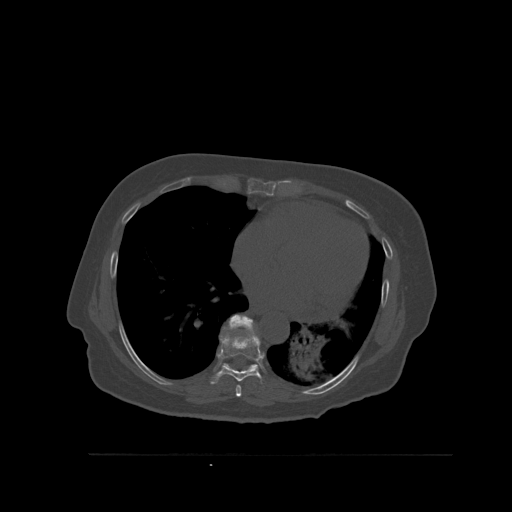
CT including the spine, one axial slice. Position 348 of 527 along the scan axis. Bone window (W 1800 / L 400 HU). 1.5 mm slice thickness. 512 × 512 image matrix, field of view 470 × 470 mm. Patient: female, 73 years. Case-level facts recorded for this patient, not image findings: primary cancer: breast; vertebrae with lytic lesions (as recorded): L2.
Outlined on this slice (semi-automatic segmentation, software-assisted and operator-edited):
- T7 vertebra: box from (x=235, y=385) to (x=242, y=397) px
- T8 vertebra: (x=210, y=328)–(x=262, y=385)
- T9 vertebra: (x=223, y=315)–(x=259, y=371)